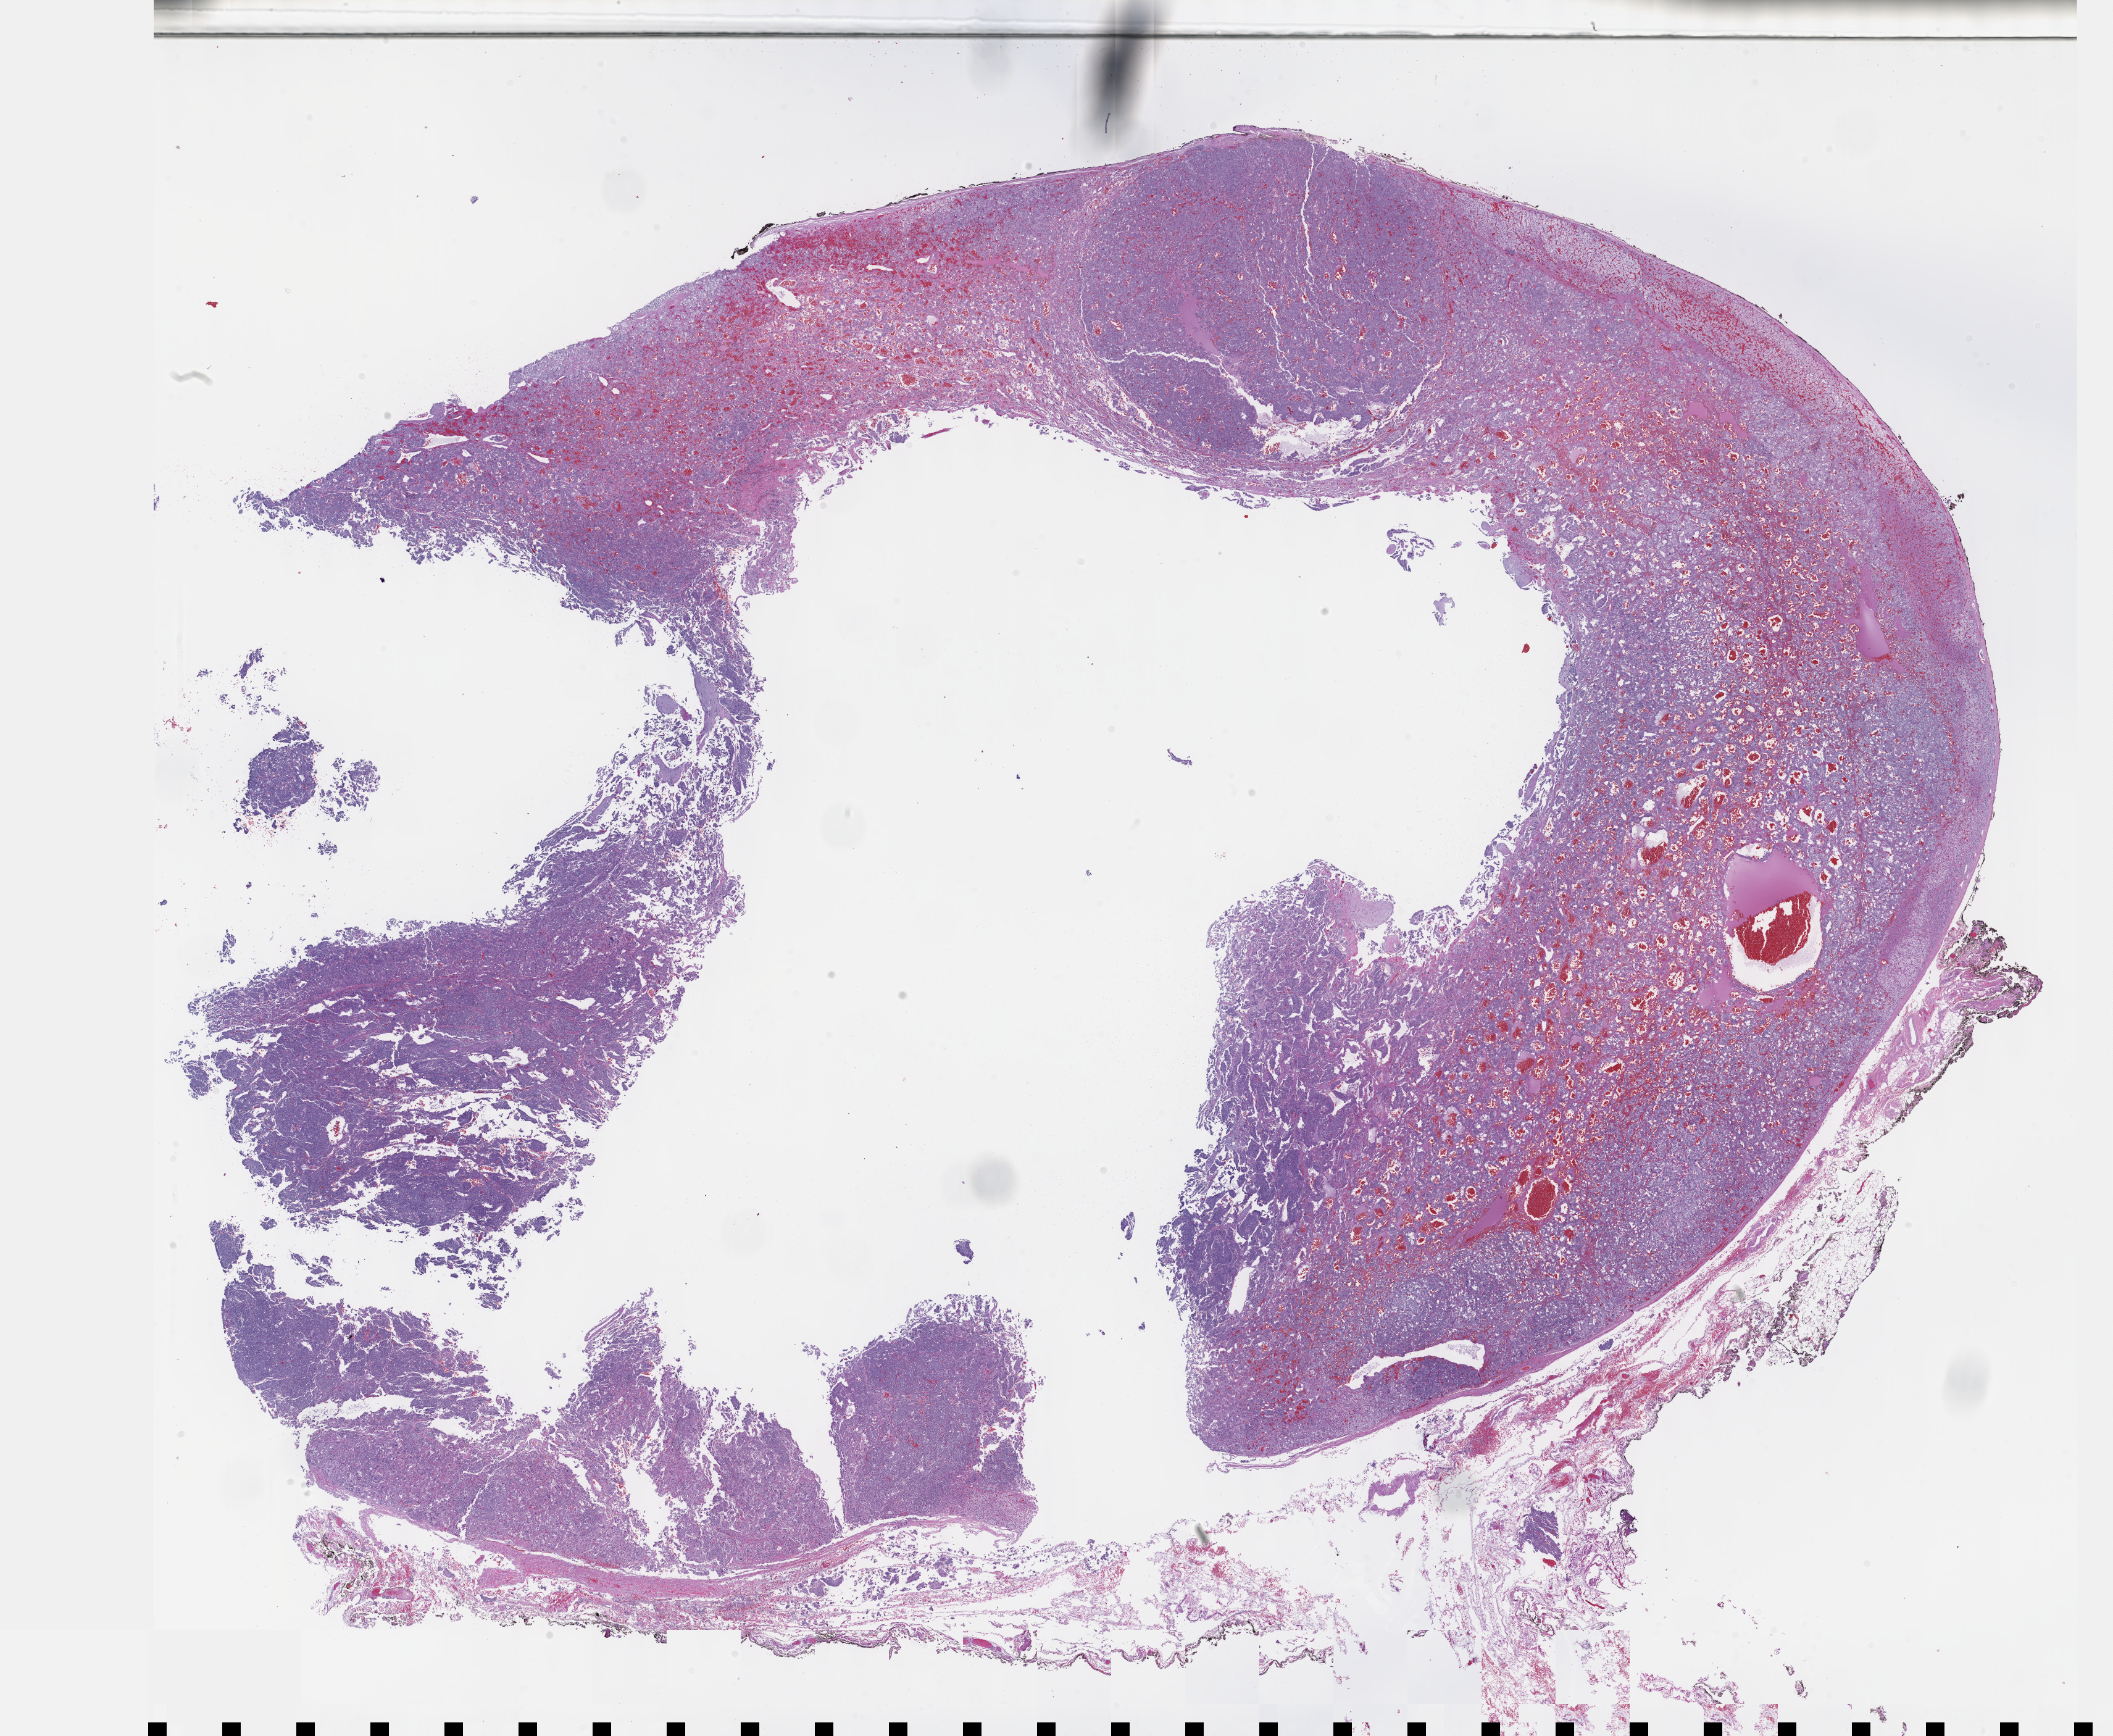
Digitized Hematoxylin and eosin (H&E) stained tissue section (whole slide) — whole scanned area (about 27.7 x 22.7 mm) shown as a low-resolution overview, formalin-fixed paraffin-embedded (FFPE) diagnostic section, adrenal gland, primary tumour sample. Patient: female, age at initial diagnosis 46 years.
Histologic diagnosis: Pheochromocytoma, NOS.